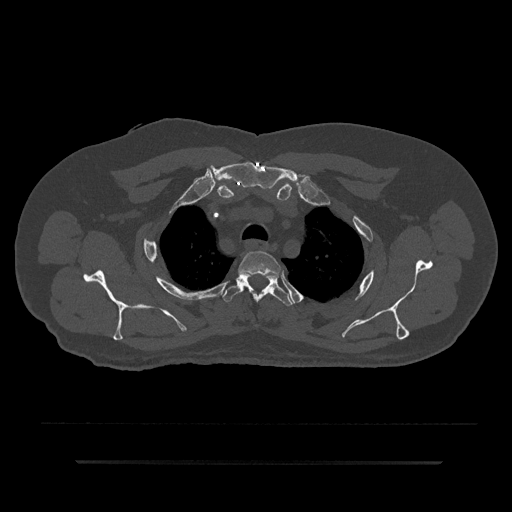
CT including the spine, one axial slice; slice 674 of 797 in the series (ordered by position); bone window (W 1800 / L 400 HU); 512 × 512 image matrix. Patient: male, 59 years. Case-level facts recorded for this patient, not image findings: primary cancer: bile ducts; vertebrae with lytic lesions (as recorded): T10.
Structures marked on this image (semi-automatic segmentation, software-assisted and operator-edited):
- T2 vertebra: bounding box <238,251,281,276> (left, top, right, bottom; pixels)
- T3 vertebra: <223,273,293,306>